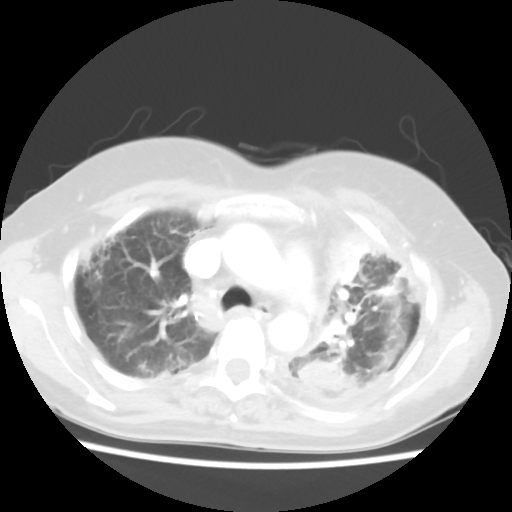
Chest CT, one axial slice. Slice 40 of 56 in the series (ordered by position). Lung window (W 1500 / L -600 HU). 512 × 512 image matrix, field of view 309 × 309 mm. Patient: female, 56 years. Case-level facts recorded for this patient, not image findings: clinical TNM (as recorded): T1c N0 M1.
Structures marked on this image (rectangle marked by the reading radiologist):
- lung tumour (recorded histology: adenocarcinoma): bounding box [x1, y1, x2, y2] px = [325, 233, 366, 288]